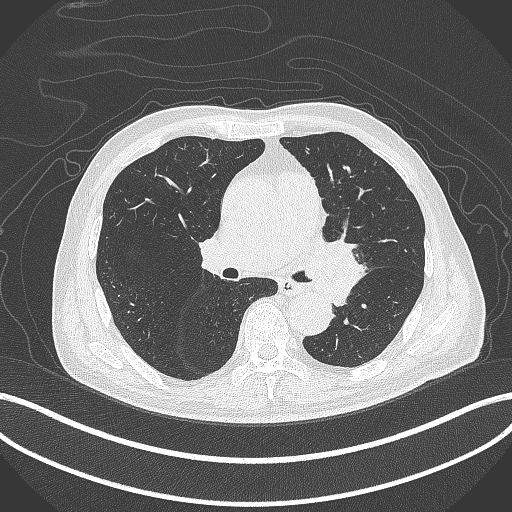
Chest CT, one axial slice. Slice 246 of 417 in the series (ordered by position). Reconstruction kernel B70f. Lung window (W 1500 / L -600 HU). 1 mm slice thickness. 512 × 512 image matrix, field of view 400 × 400 mm. Male patient, age 77 years. From the clinical record (not read from this slice): clinical TNM (as recorded): T3 N1 M0.
Structures marked on this image (bounding box drawn by a radiologist):
- lung tumour (recorded histology: adenocarcinoma): bounding box <306,234,366,307> (left, top, right, bottom; pixels)